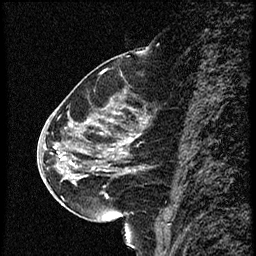
Breast MRI (dynamic contrast-enhanced), one sagittal slice. Slice 27 of 56 in the series (ordered by position). Dynamic contrast-enhanced study with each time point stored as its own series, time point 2 of 4 at this slice position (early post-contrast, ordered by acquisition time). 1.5 T. TE 4.2 ms, TR 18.9 ms. 256 × 256 image matrix, field of view 200 × 200 mm. Female patient. Case-level facts recorded for this patient, not image findings: setting: breast cancer imaged before/during neoadjuvant chemotherapy; receptor status: HER2-positive.
Annotated regions visible in this slice (semi-automatic segmentation, software-assisted and operator-edited):
- analysis volume of interest (the breast-tissue region the enhancement analysis was run in; not a lesion): box from (x=63, y=80) to (x=166, y=215) px
- tumour enhancement mask (voxels above the 100 % enhancement threshold inside the analysis volume of interest): (x=65, y=138)–(x=134, y=185)